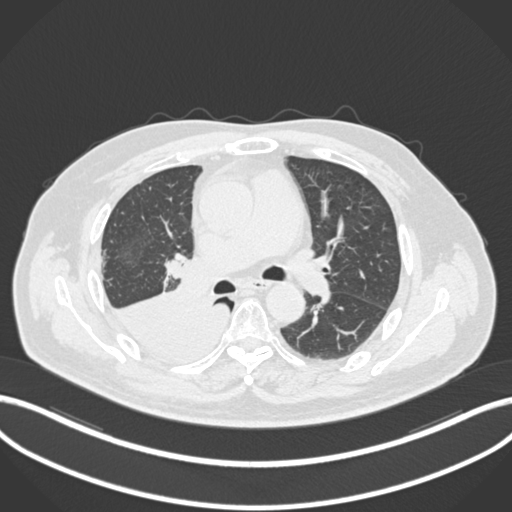
Chest CT, one axial slice; position 114 of 218 along the scan axis; lung window (W 1500 / L -600 HU); 1 mm slice thickness; 512 × 512 image matrix, field of view 400 × 400 mm. Male patient, age 68 years. Case-level facts recorded for this patient, not image findings: clinical TNM (as recorded): T2a N0 M0.
Outlined on this slice (rectangle marked by the reading radiologist):
- lung tumour (recorded histology: adenocarcinoma): bounding box (x1, y1, x2, y2) in pixels: (108, 291, 230, 364)